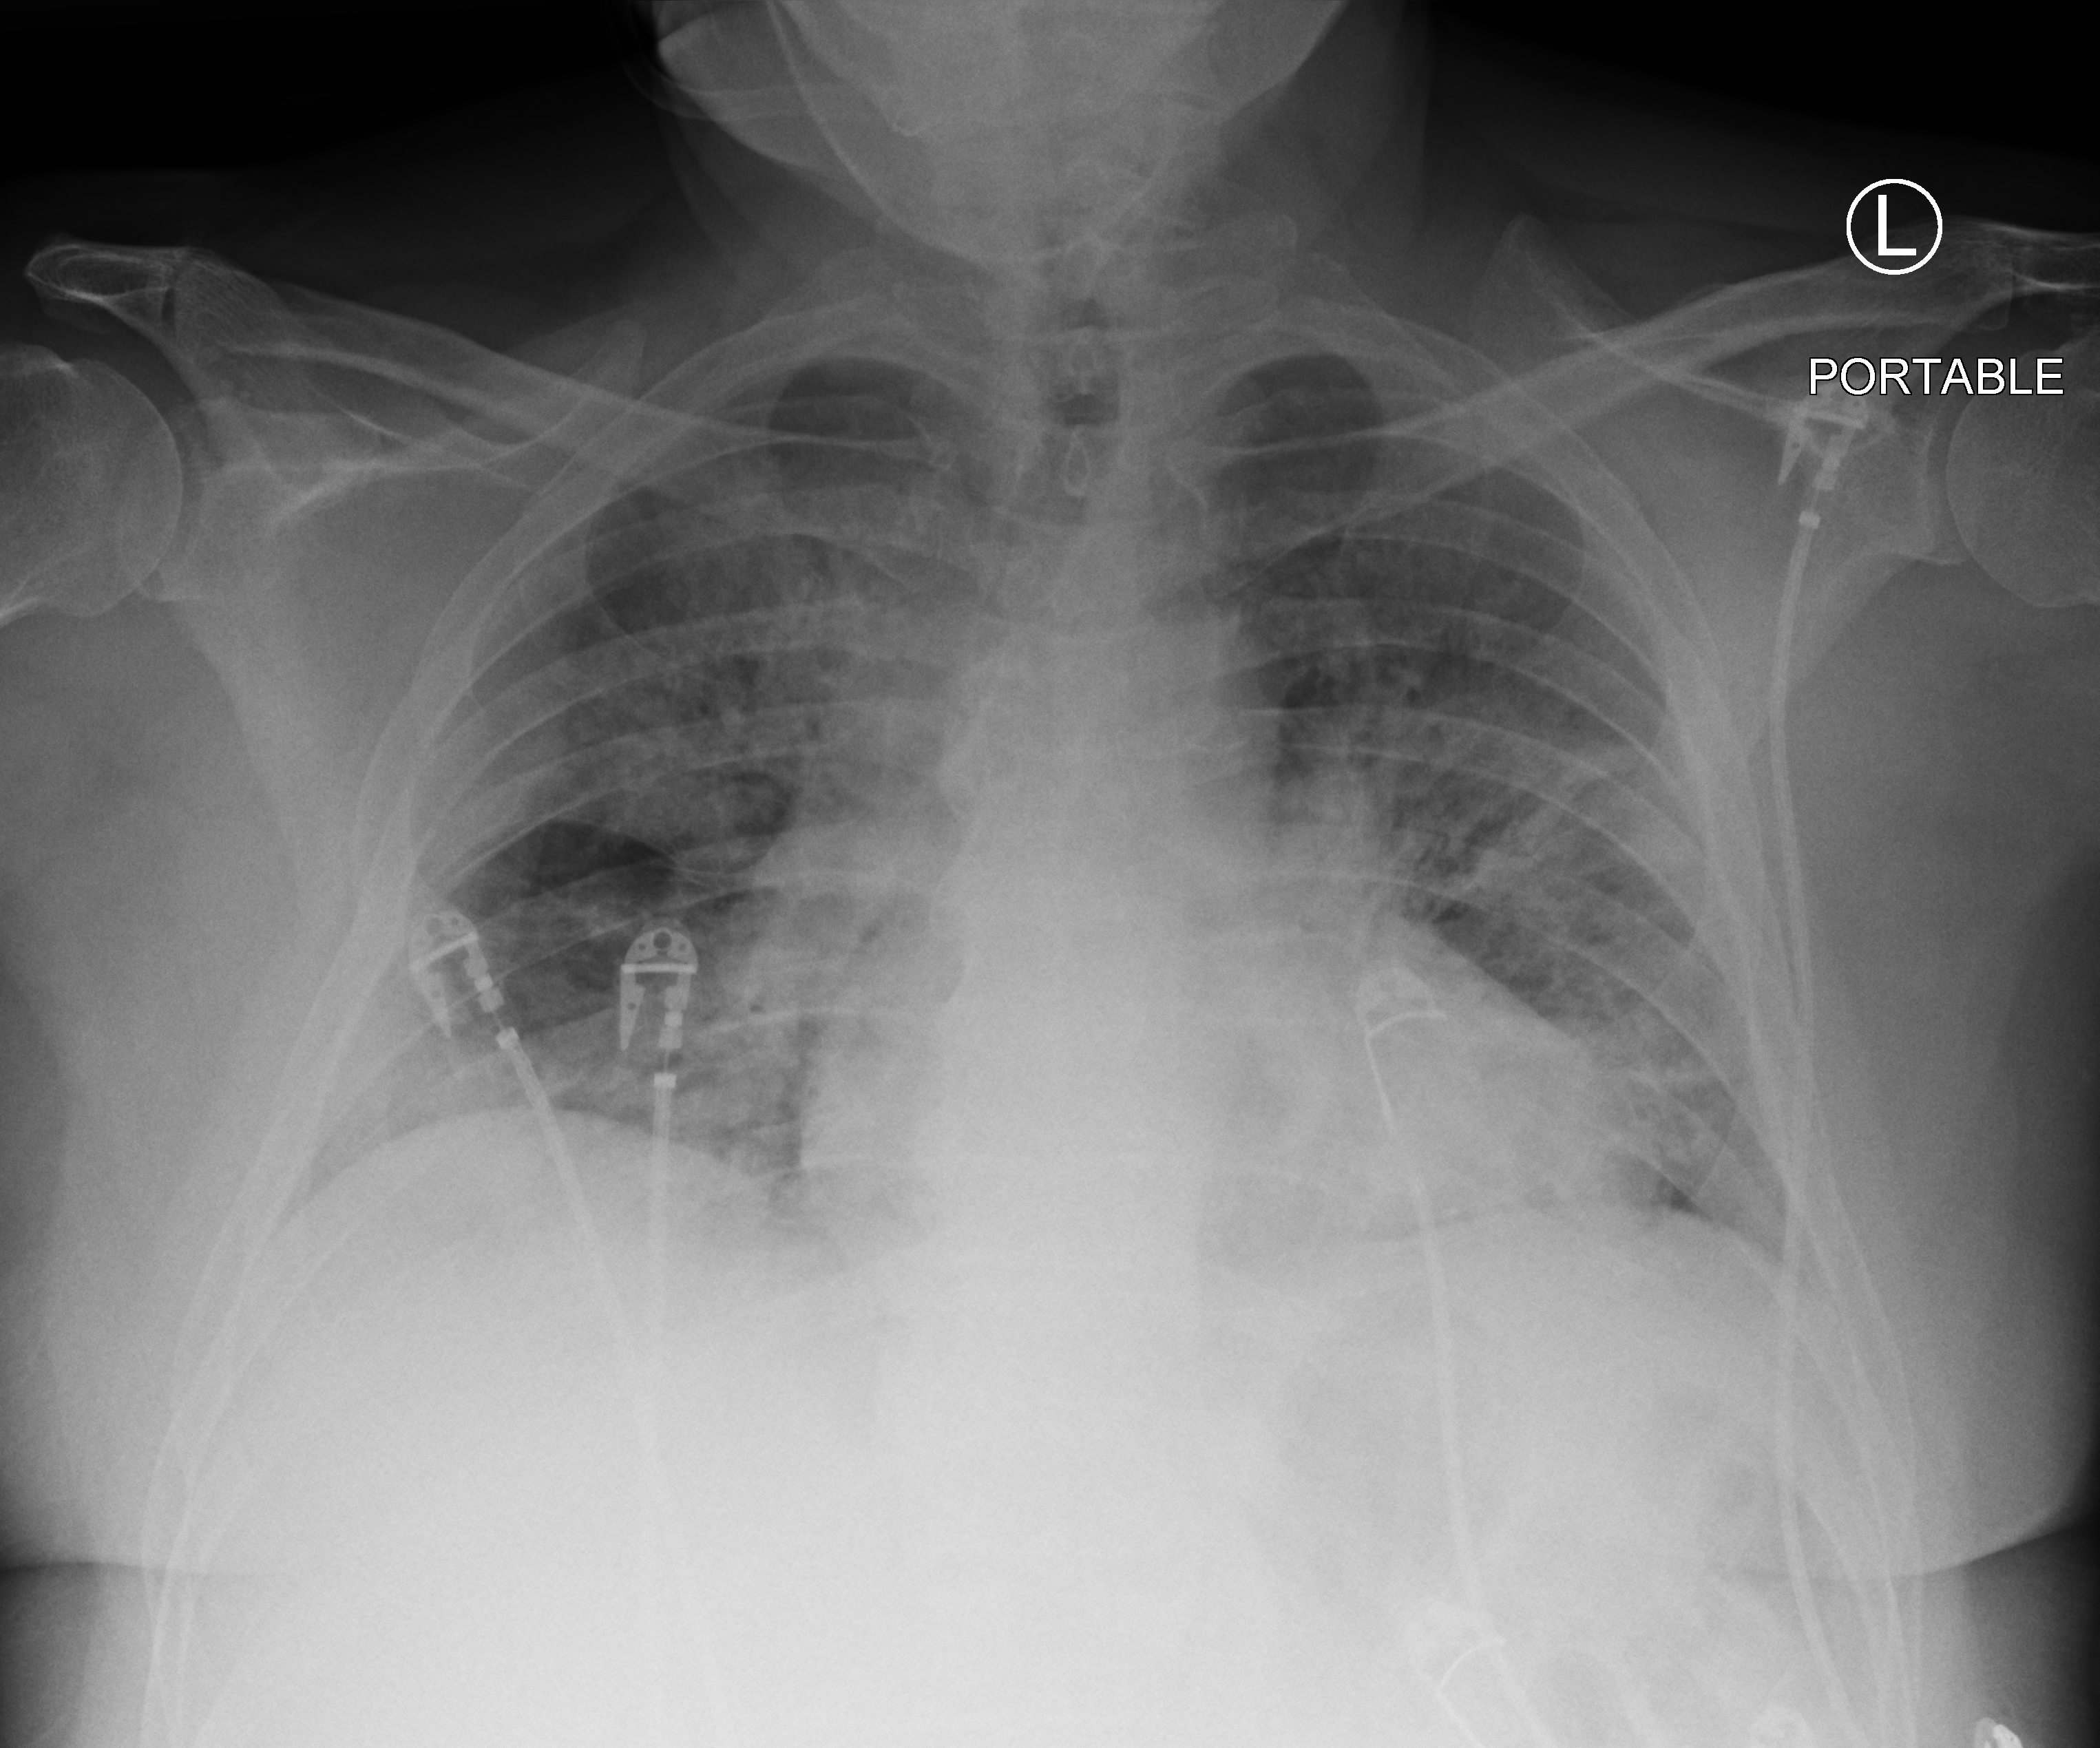
Bedside chest radiograph (computed radiography). Patient hospitalised with COVID-19; male, aged 60–74 years.
Hospital-stay facts (about this admission, not read from this image; timing relative to this image not recorded): length of hospital stay: 15 days; chronic kidney disease (admission record): no; admitted to intensive care during this hospital stay: yes.